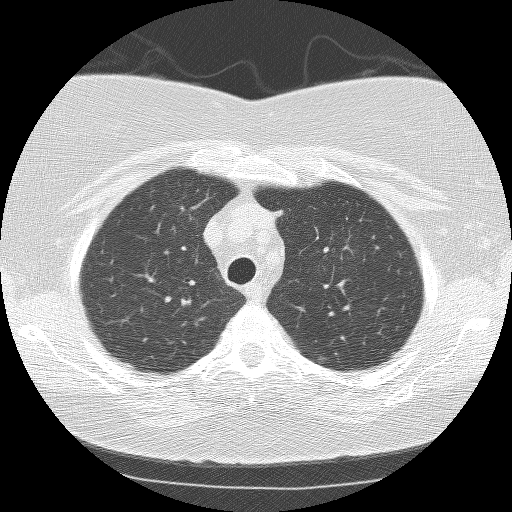
Chest CT (low-dose screening protocol), one axial image, first (baseline) screen, lung window (W 1500 / L -600 HU), lung (sharp) reconstruction kernel (BONE), 120 kVp, slice 28 of 159 in the series, 512 × 512 image matrix. Female, age 64 years at enrolment. Current smoker at enrolment.
• Lesion marked by an expert reader, bounding box [x1, y1, x2, y2] px = [162, 284, 206, 322].
• Screening reader's record for this exam (one nodule recorded; not confirmed to be the boxed lesion): non-calcified nodule or mass ≥4 mm, right upper lobe, 7 × 7 mm, smooth margins, soft tissue attenuation.
• Official screen result: positive, change unspecified: nodule(s) >= 4 mm or enlarging nodule(s), mass(es), or other non-specific abnormalities suspicious for lung cancer.
• Later outcome: lung cancer diagnosed 314 days after this screen — small cell carcinoma, NOS, right hilum, stage IV (AJCC 6th edition).